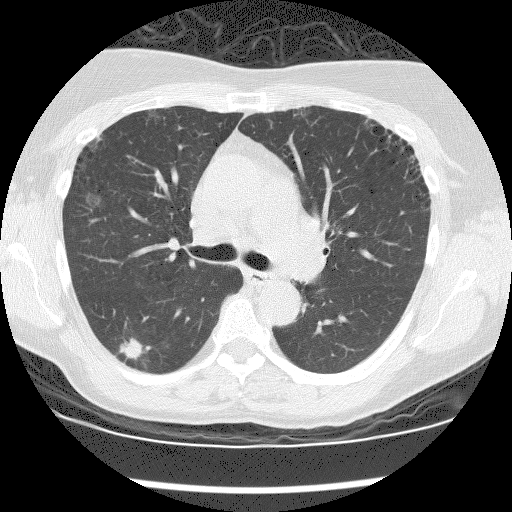
Low-dose screening chest CT, axial slice. First (baseline) screen. Lung window (W 1500 / L -600 HU). Lung (sharp) reconstruction kernel (BONE). Slice 59 of 176 in the series. 512 × 512 image matrix. Female participant, aged 59 years at enrolment. Current smoker at enrolment.
Lesion marked by an expert reader, bounding box [x1, y1, x2, y2] px = [110, 339, 149, 371]. The screening reader recorded 6 non-calcified nodules or masses ≥4 mm on this exam (right upper lobe, right upper lobe, right lower lobe, right lower lobe, right upper lobe, right upper lobe); which of them this box marks is not recorded. Participant outcome: lung cancer diagnosed 242 days after this screen — adenocarcinoma, NOS, right lower lobe, moderately differentiated (G2), stage IIIA (AJCC 6th edition), 12 mm at pathology.